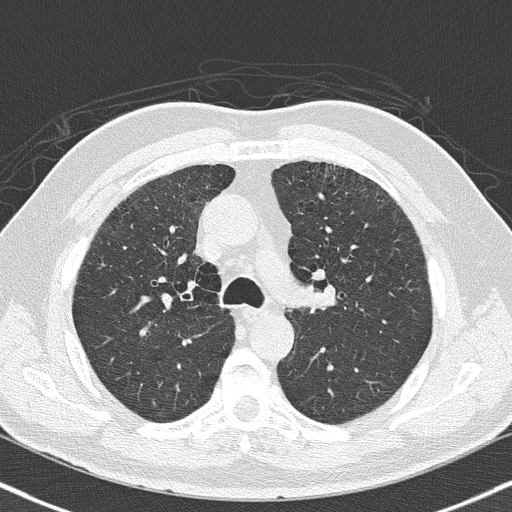
Axial slice from a low-dose chest CT screening exam, second screening round (one year after baseline), lung window (W 1500 / L -600 HU), 2 mm slice thickness, 512 × 512 image matrix, field of view 324 × 324 mm. Male participant, aged 64 years at enrolment. Current smoker at enrolment.
Lesion marked by an expert reader, bounding box <313,274,348,308> (left, top, right, bottom; pixels). Screening reader's record for this exam: no non-calcified nodule ≥4 mm recorded. Official screen result: positive, other. Later outcome: lung cancer diagnosed 72 days after this screen — squamous cell carcinoma, keratinizing, NOS, left upper lobe, moderately differentiated (G2), stage IA (AJCC 6th edition), 4 mm at pathology.